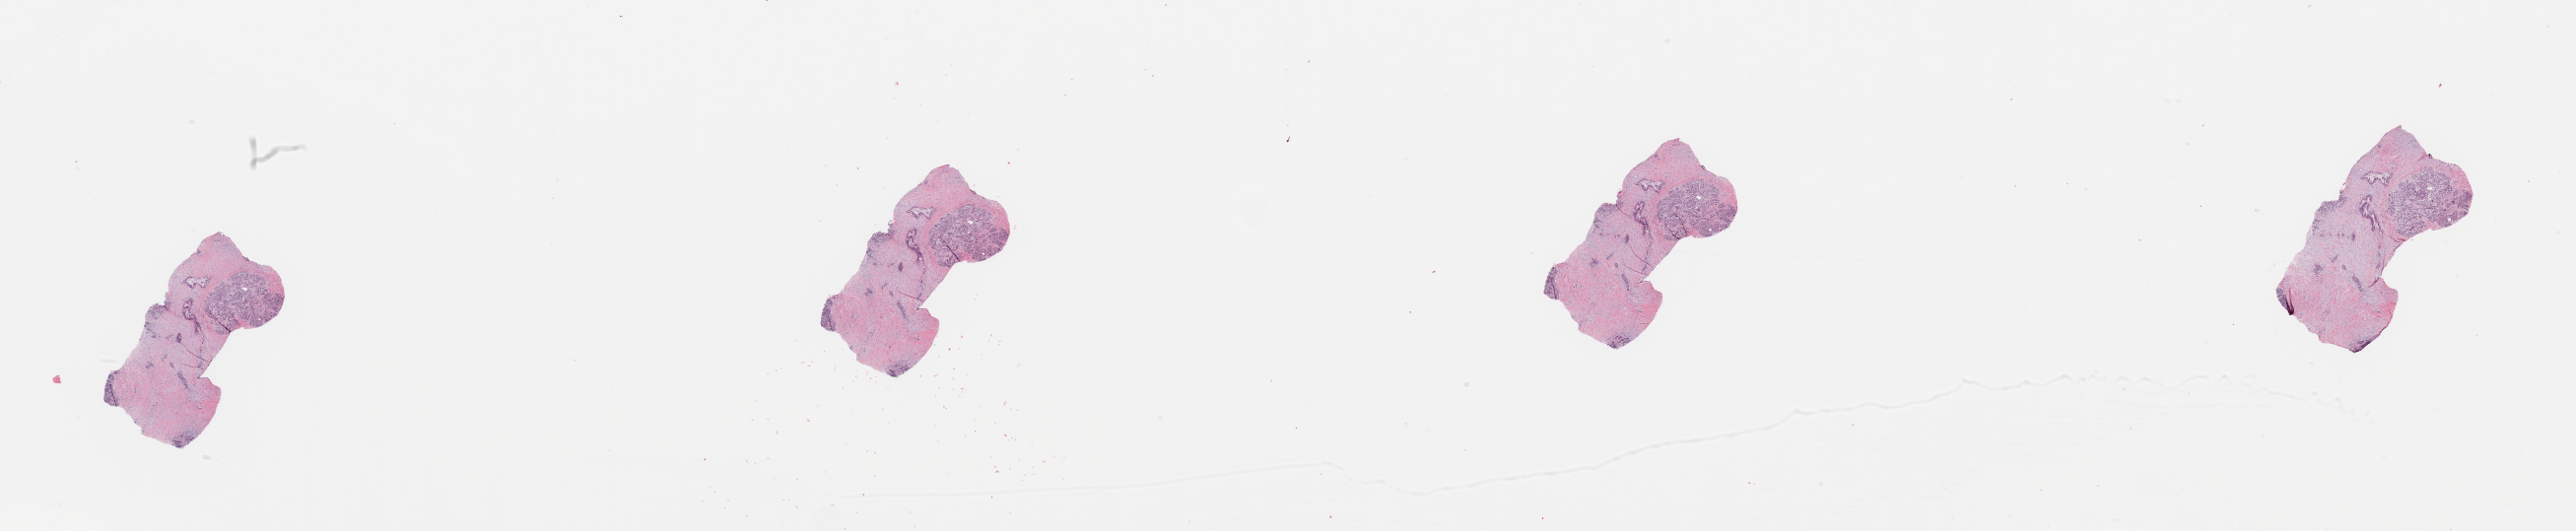
H&E-stained whole-slide image — shown as a low-resolution overview of the whole scanned area (about 41.3 x 8.5 mm), pancreas, tumour tissue. Female, 69 y/o. Histologic grade: G2 (moderately differentiated).
- histologic diagnosis: Infiltrating duct carcinoma, NOS
- AJCC pathologic stage: IIB
- primary tumour site (as recorded): head